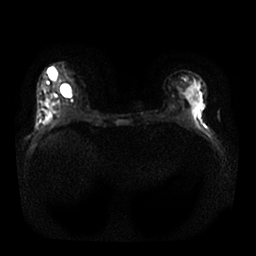
Breast MRI, one axial slice; slice 13 of 25 in the series (ordered by position); diffusion-weighted series; image 2 of 4 stored at this slice position (different b-values; order by instance number); 1.5 T; 256 × 256 image matrix, field of view 340 × 340 mm. Female patient.
Annotated regions visible in this slice (outlined manually by an expert reader):
- tumour on diffusion-weighted imaging: bounding box [x1, y1, x2, y2] px = [184, 75, 201, 105]